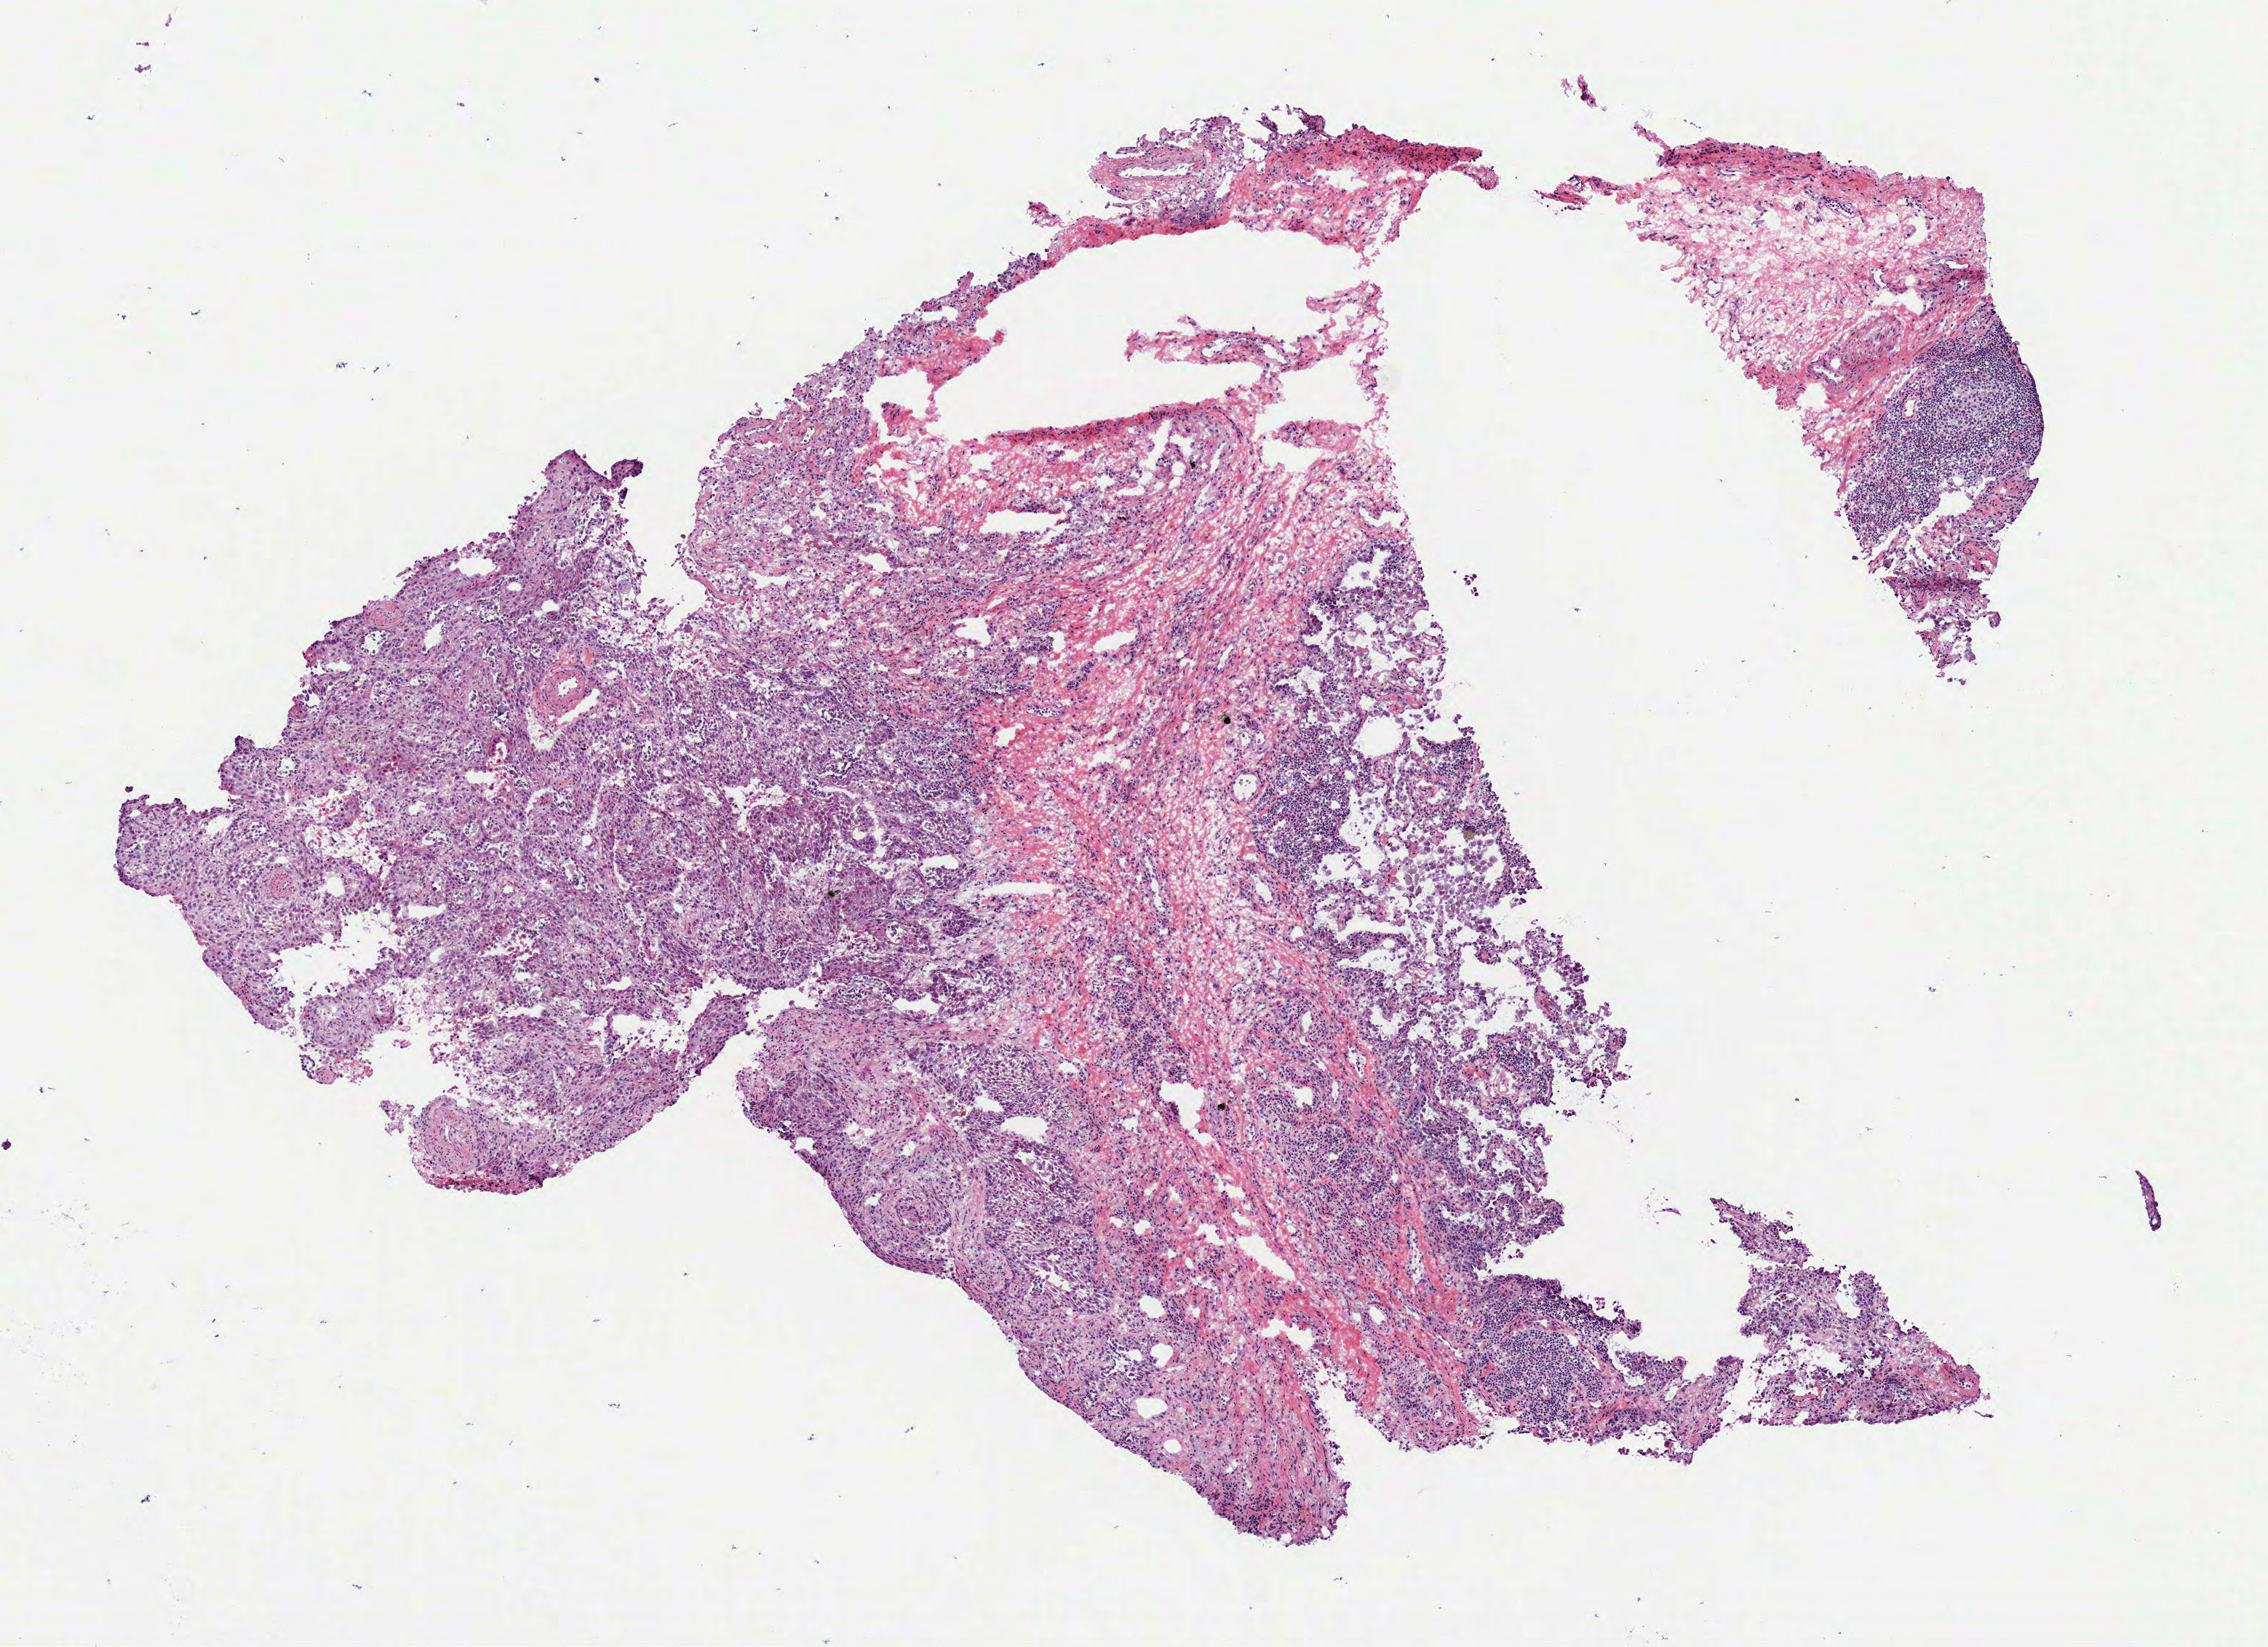
Digitized H&E tissue section (whole slide), whole scanned area (about 6.3 x 4.6 mm, from a 40x scan) shown as a low-resolution overview; frozen section; primary tumour sample from the lung. Male, age 73 years at initial diagnosis. Pathologist review of this section (percent, as recorded): tumour cells 65%, tumour nuclei 65%, normal cells 0%, stromal cells 32%, necrosis 3%. Infiltration values recorded for this section: lymphocyte infiltration 20%, monocyte infiltration 2%, neutrophil infiltration 2%.
* laterality: right
* pathologic diagnosis: Squamous cell carcinoma, NOS (lower lobe, lung)
* AJCC pathologic stage: IA